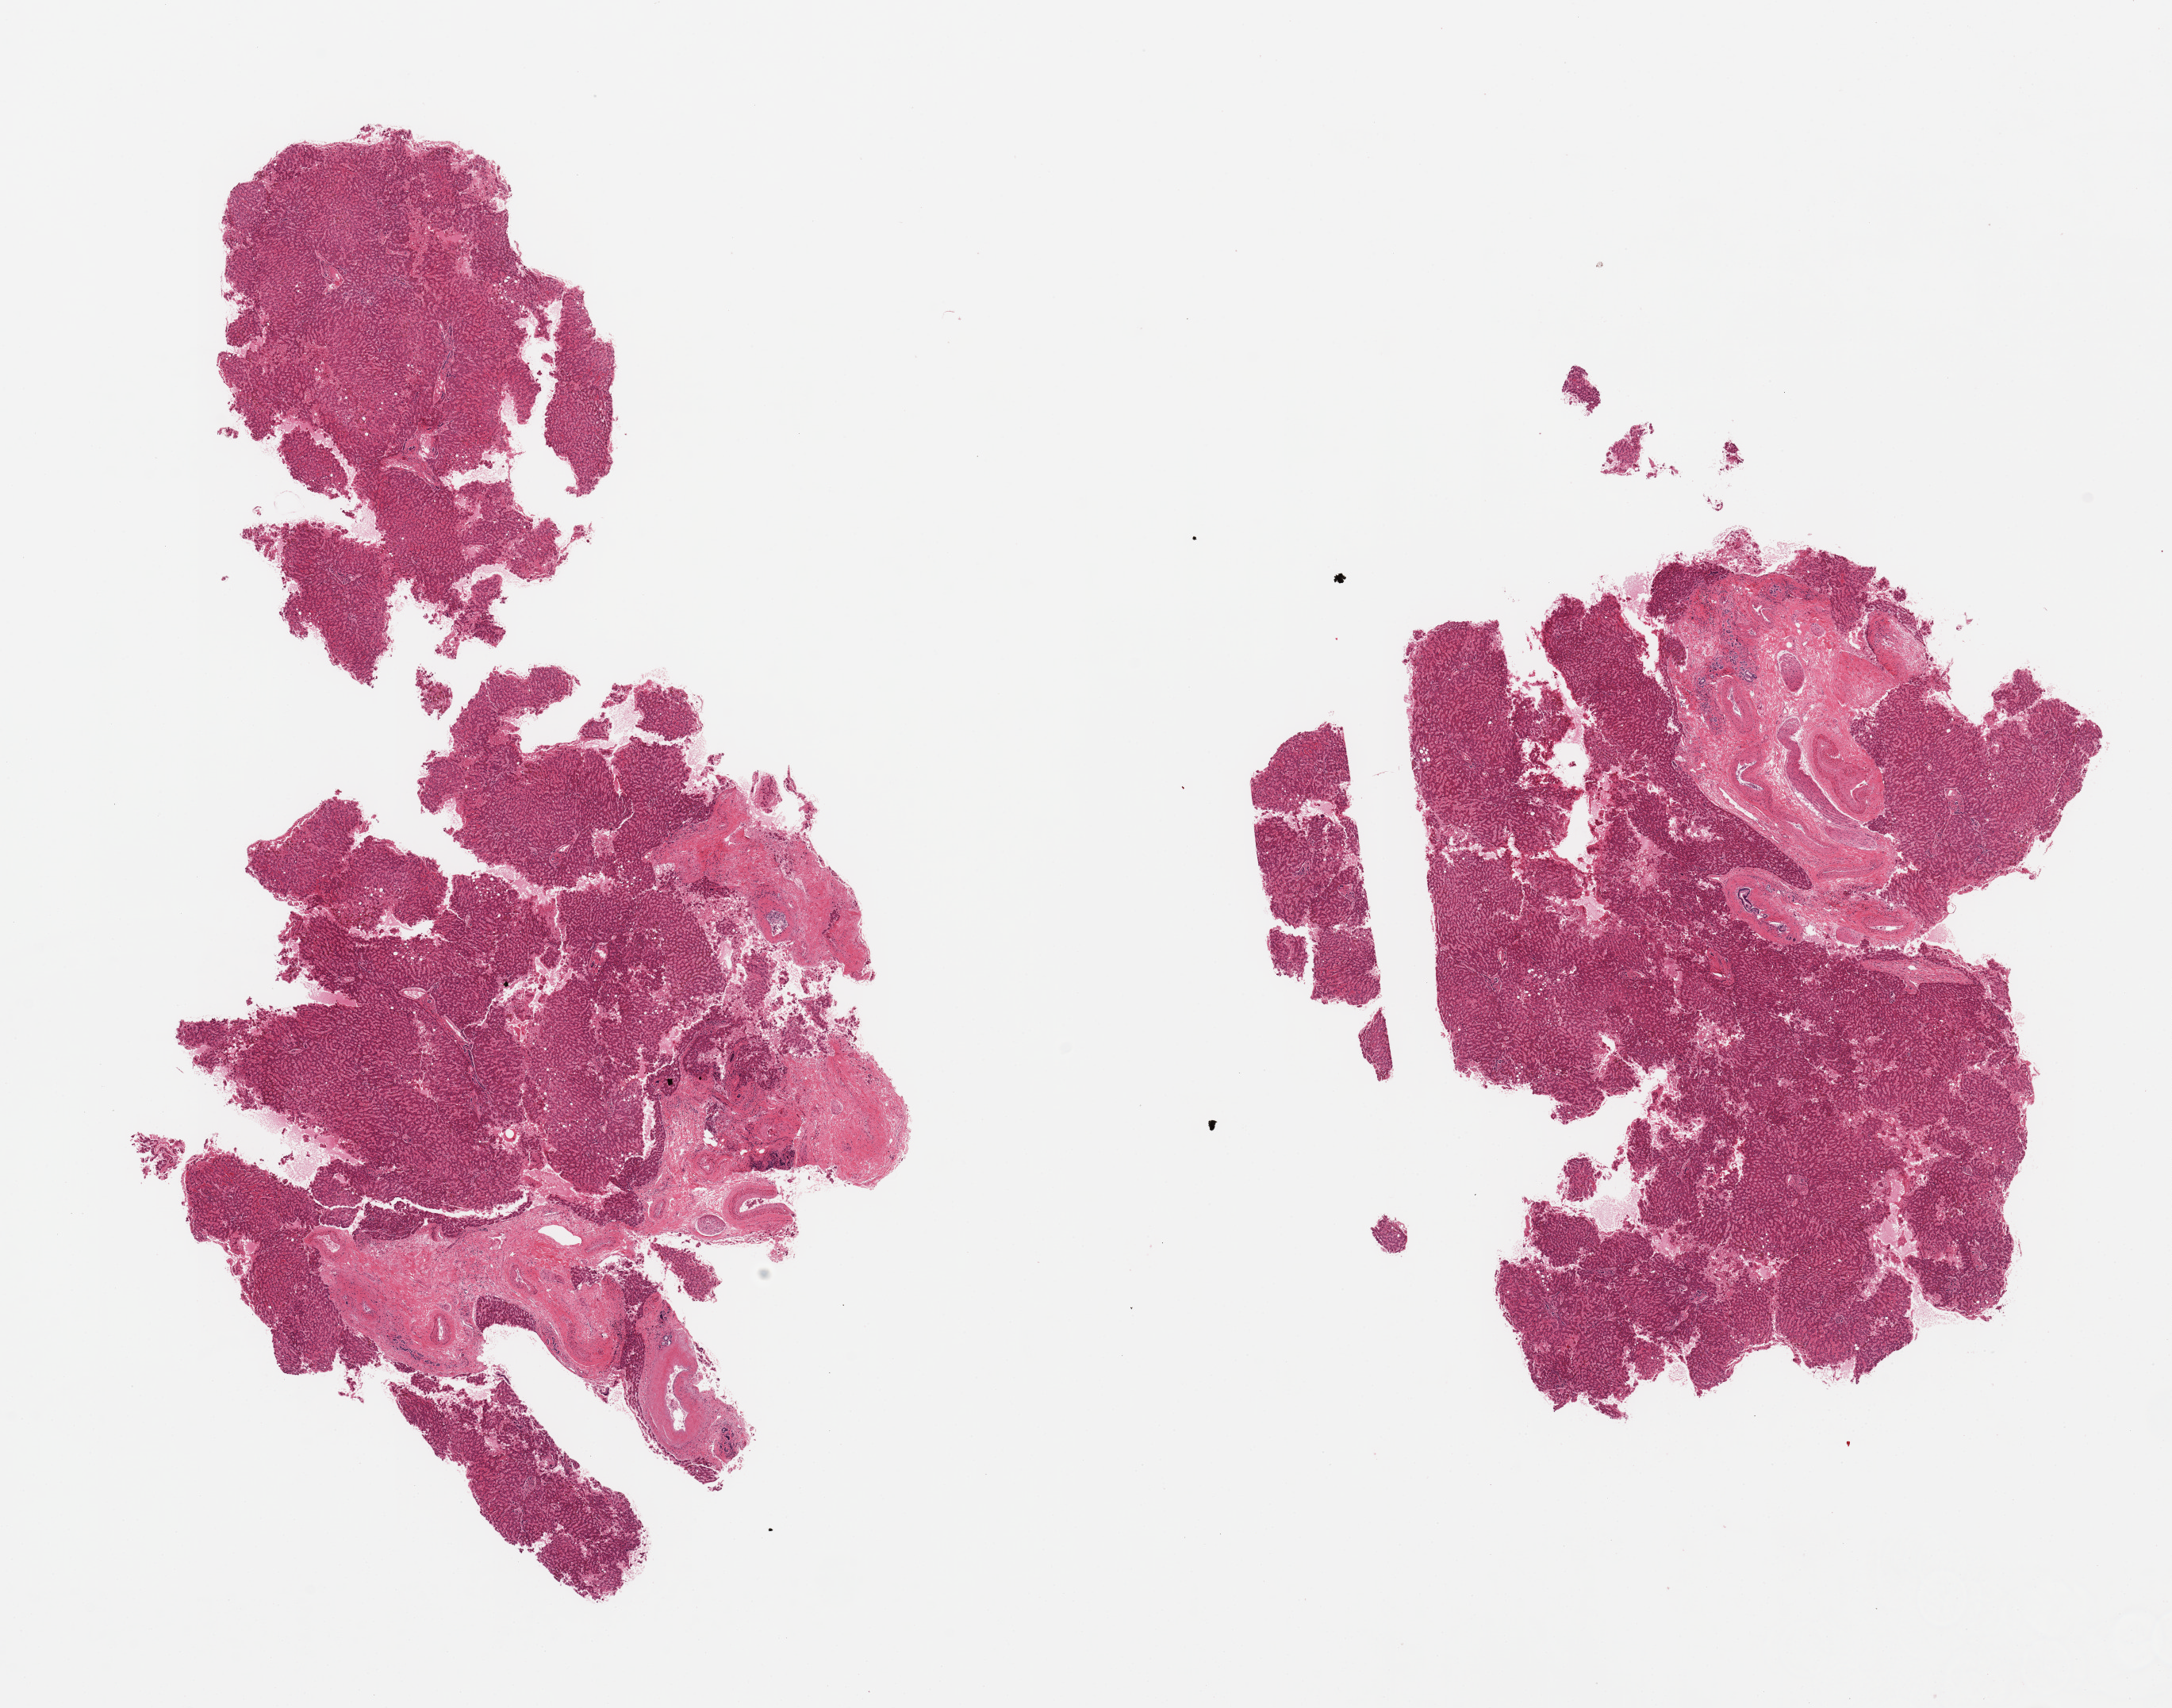
H&E whole-slide image, brightfield — shown as a low-resolution overview of the whole scanned area (about 21.7 x 17.0 mm, slide scanned at 20x). PAXgene-fixed paraffin-embedded (PFPE) section. Target tissue: liver. Tissue donor sample. Donor sex: female.
Reviewer comment on this tissue sample: 2 fragmented pieces; 20% of each consists of large vessels & nerves.